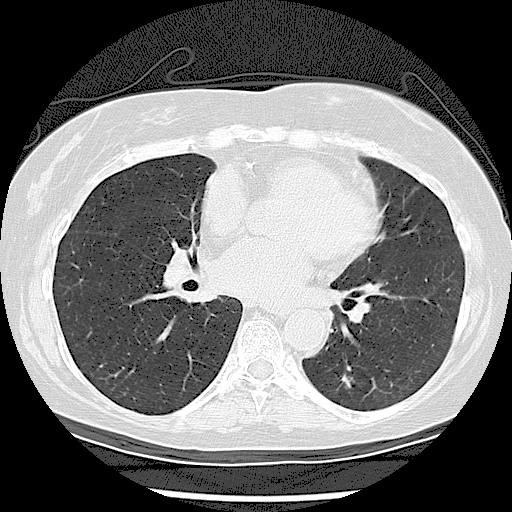
Low-dose screening chest CT, axial slice; baseline annual screen; lung window (W 1500 / L -600 HU); 2.5 mm slice thickness; 512 × 512 image matrix. Female participant, aged 61 years at enrolment. Current smoker at enrolment.
• Lesion marked by an expert reader, bounding box [x1, y1, x2, y2] px = [323, 358, 369, 406].
• The screening reader recorded 2 non-calcified nodules or masses ≥4 mm on this exam (left lower lobe, right lower lobe); which of them this box marks is not recorded.
• Later outcome: lung cancer diagnosed 570 days after this screen — adenocarcinoma, NOS, left lower lobe, moderately differentiated (G2), stage IA (AJCC 6th edition), 18 mm at pathology.